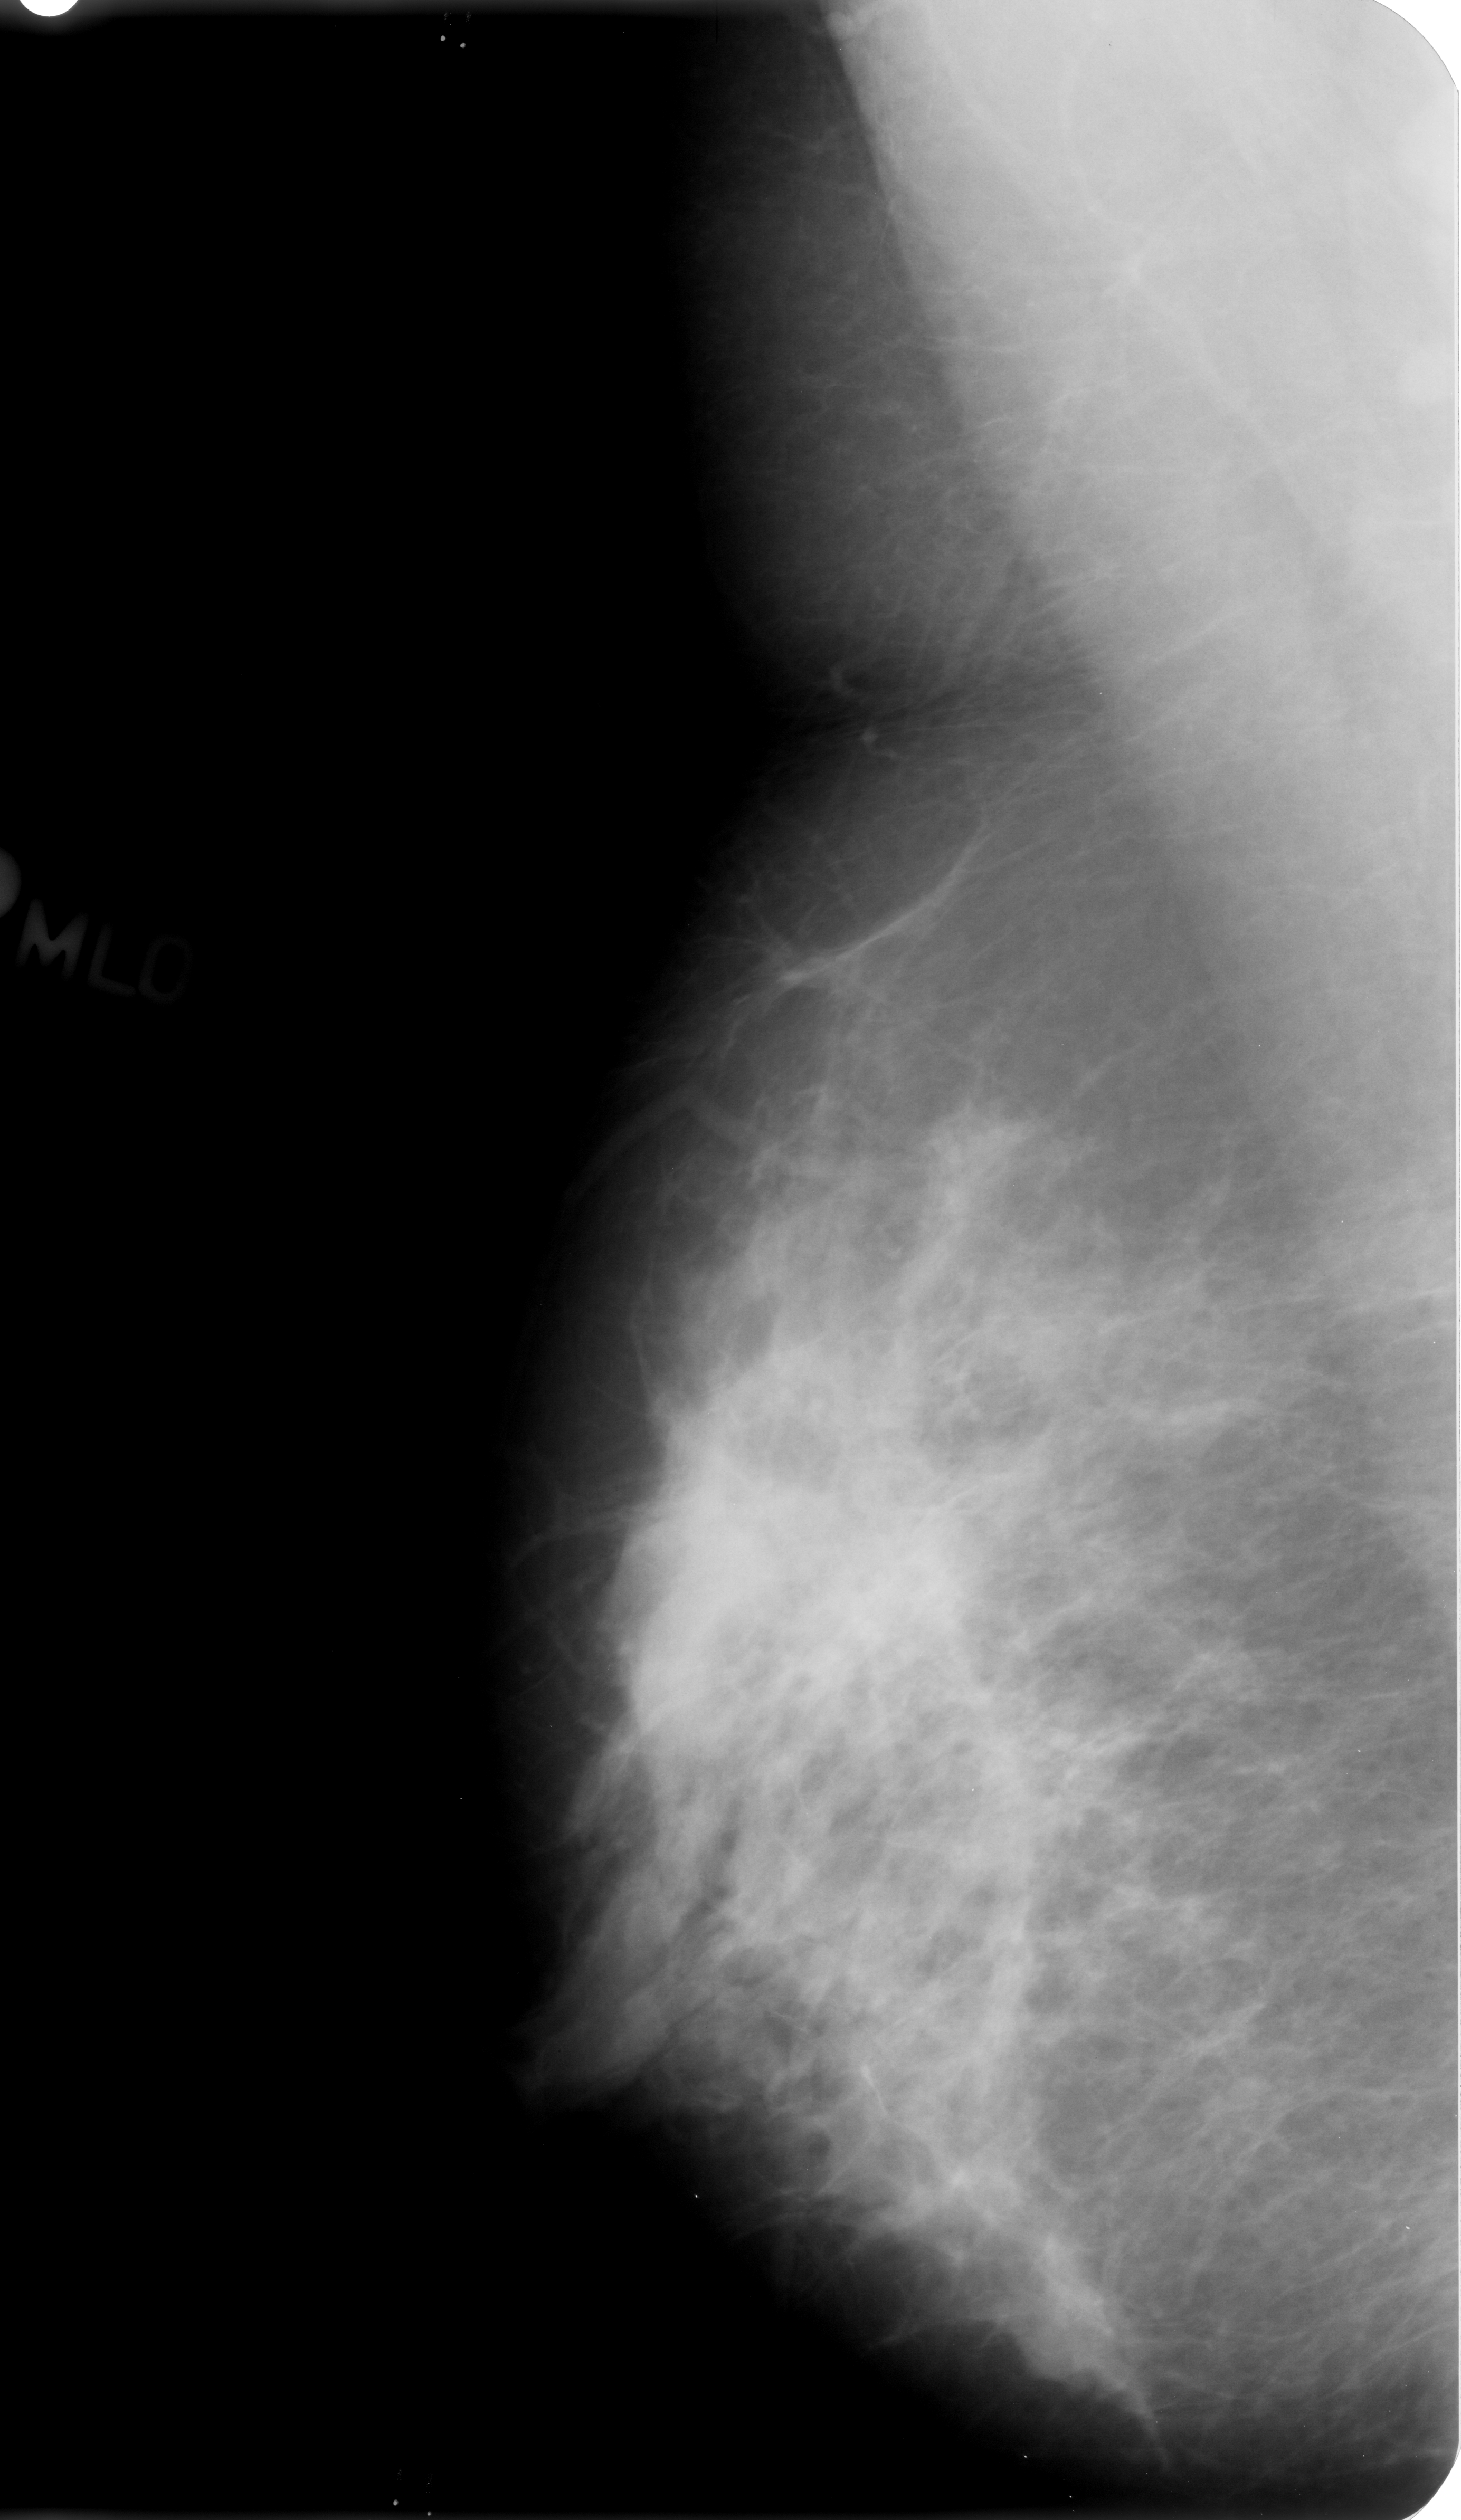
Mammogram (digitized film), right breast, MLO view, breast composition: heterogeneously dense (BI-RADS density category 3 of 4).
Finding: mass, shape irregular, margins ill defined / spiculated; BI-RADS assessment category 4; subtlety rating 3 on a 1 (subtle) to 5 (obvious) scale; pathology (as recorded): benign.